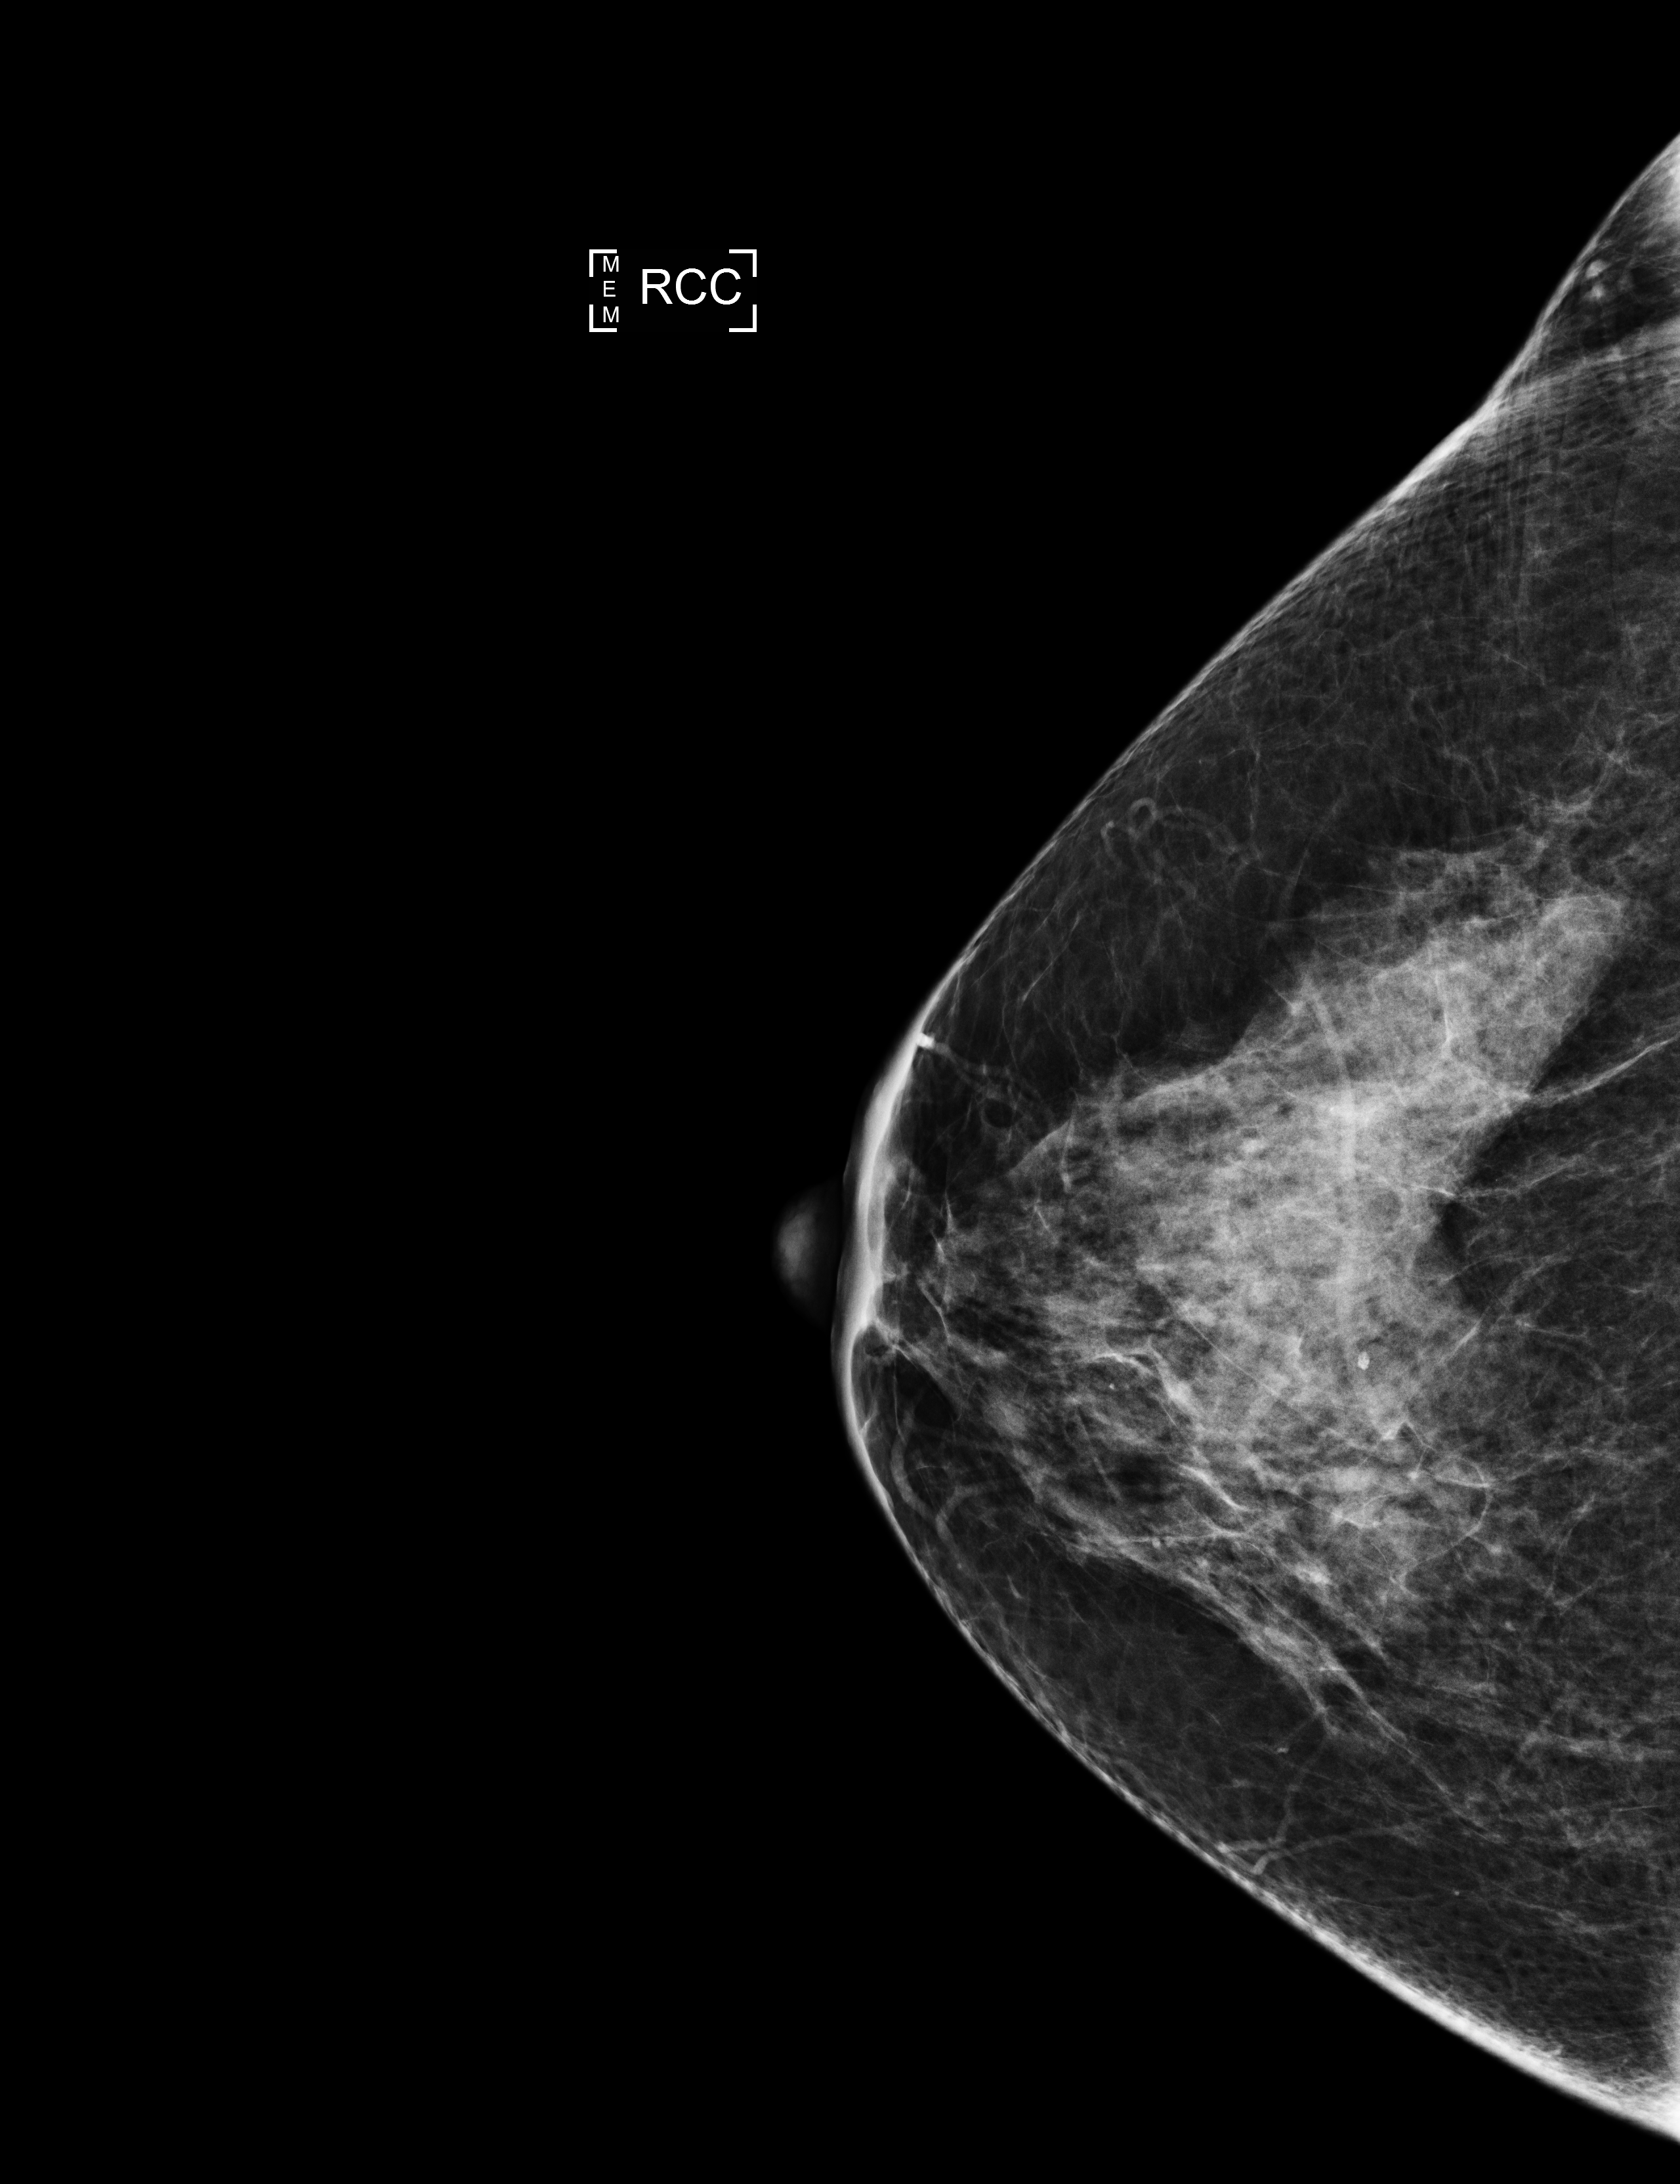
Full-field digital mammogram (FFDM), right breast, craniocaudal (CC) view, annual screening mammography examination, compressed breast thickness 59 mm, system: Selenia Dimensions. Patient: female, 57 years.
BI-RADS breast density category at the screening exam (both breasts, scale 1–4): 3. Final BI-RADS assessment for this screening round (tomosynthesis exam, both breasts): category 1. Recall: no recall after this screen.